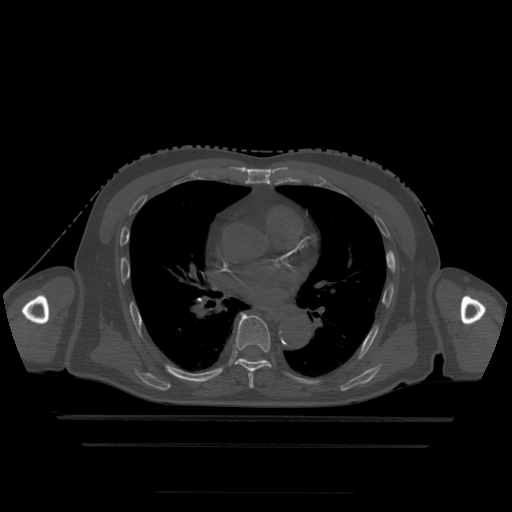
CT including the spine, one axial slice. Position 299 of 522 along the scan axis. Bone window (W 1800 / L 400 HU). 1.25 mm slice thickness. 512 × 512 image matrix, field of view 436 × 436 mm. Patient age 68 years. From the clinical record (not read from this slice): primary cancer: urothelial.
Annotated regions visible in this slice (semi-automatically segmented with operator editing):
- T6 vertebra: bounding box <248,374,254,389> (left, top, right, bottom; pixels)
- T7 vertebra: <235,313,271,374>